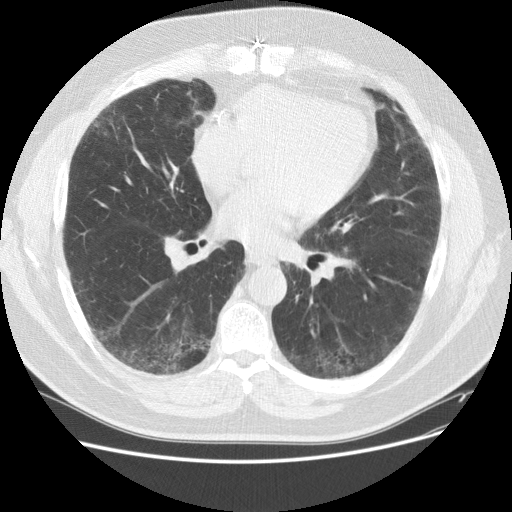
Axial slice from a low-dose chest CT screening exam; first (baseline) screen; lung window (W 1500 / L -600 HU); 120 kVp; slice 74 of 151 in the series; 512 × 512 image matrix, field of view 378 × 378 mm. Male participant, aged 59 years at enrolment. Current smoker at enrolment.
• Lesion marked by an expert reader, bounding box <83,96,132,146> (left, top, right, bottom; pixels).
• The screening reader recorded 2 non-calcified nodules or masses ≥4 mm on this exam (right middle lobe, right lower lobe); which of them this box marks is not recorded.
• Official screen result: positive, change unspecified: nodule(s) >= 4 mm or enlarging nodule(s), mass(es), or other non-specific abnormalities suspicious for lung cancer.
• Lung cancer was diagnosed 338 days after this screen: adenocarcinoma, NOS, right upper lobe, right middle lobe, moderately differentiated (G2), stage IA (AJCC 6th edition), 13 mm at pathology.